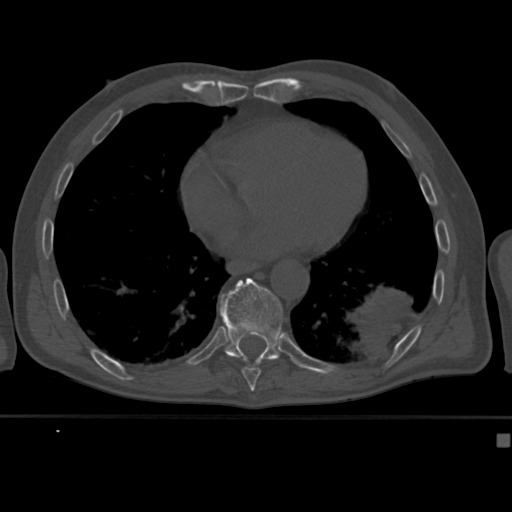
CT including the spine, one axial slice. Reconstruction kernel Br40s. 120 kVp. Bone window (W 1800 / L 400 HU). 512 × 512 image matrix, field of view 337 × 337 mm. Male patient, age 64 years. Case-level facts recorded for this patient, not image findings: primary cancer: uterus; vertebrae with lytic lesions (as recorded): T1, T4, T5, T7, L5.
Outlined on this slice (semi-automatic segmentation, software-assisted and operator-edited):
- T10 vertebra: bounding box (x1, y1, x2, y2) in pixels: (220, 278, 283, 369)
- T9 vertebra: (242, 365, 262, 382)